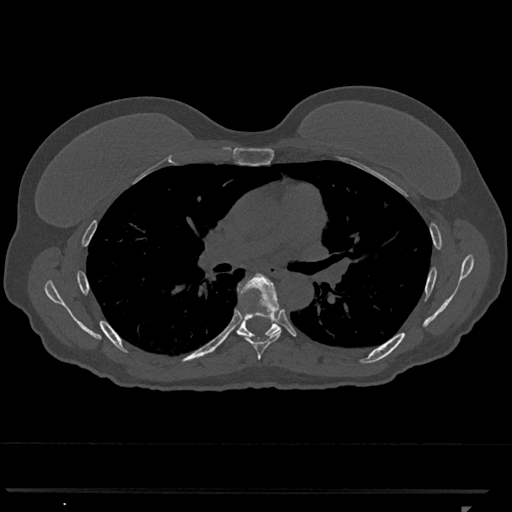
CT including the spine, one axial slice. 120 kVp. Bone window (W 1800 / L 400 HU). 0.5 mm slice thickness. 512 × 512 image matrix. Patient: female, 62 years. Case-level facts recorded for this patient, not image findings: primary cancer: renal.
Annotated regions visible in this slice (semi-automatically segmented with operator editing):
- T6 vertebra: bounding box [x1, y1, x2, y2] px = [238, 273, 281, 360]
- T7 vertebra: [235, 309, 279, 341]